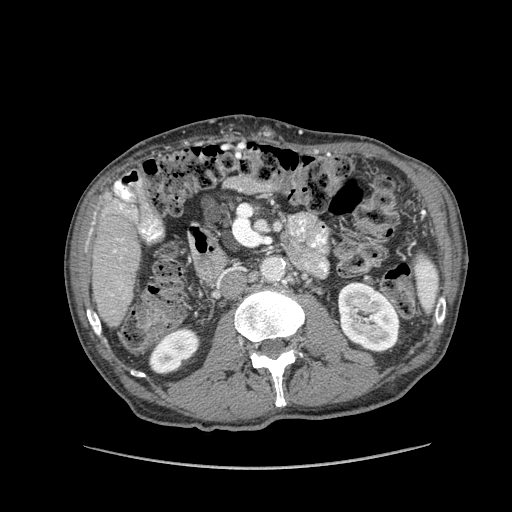
Contrast-enhanced abdominal CT (liver protocol), one axial slice; slice 23 of 162 in the series (ordered by position); reconstruction kernel STANDARD; soft-tissue window (W 400 / L 40 HU); 2.5 mm slice thickness; 512 × 512 image matrix. Case-level facts recorded for this patient, not image findings: diagnosis: hepatocellular carcinoma (patient treated with transarterial chemoembolisation; whether this scan precedes or follows treatment is not stated here); TNM stage (as recorded): Stage-IIIA; Child-Pugh class: A.
Outlined on this slice (semi-automatically segmented with operator editing):
- liver parenchyma outside the tumour (the mass and vessels are separate outlines, so this box may not span the whole liver): bounding box <92,192,140,326> (left, top, right, bottom; pixels)
- liver vessels: <113,204,129,253>